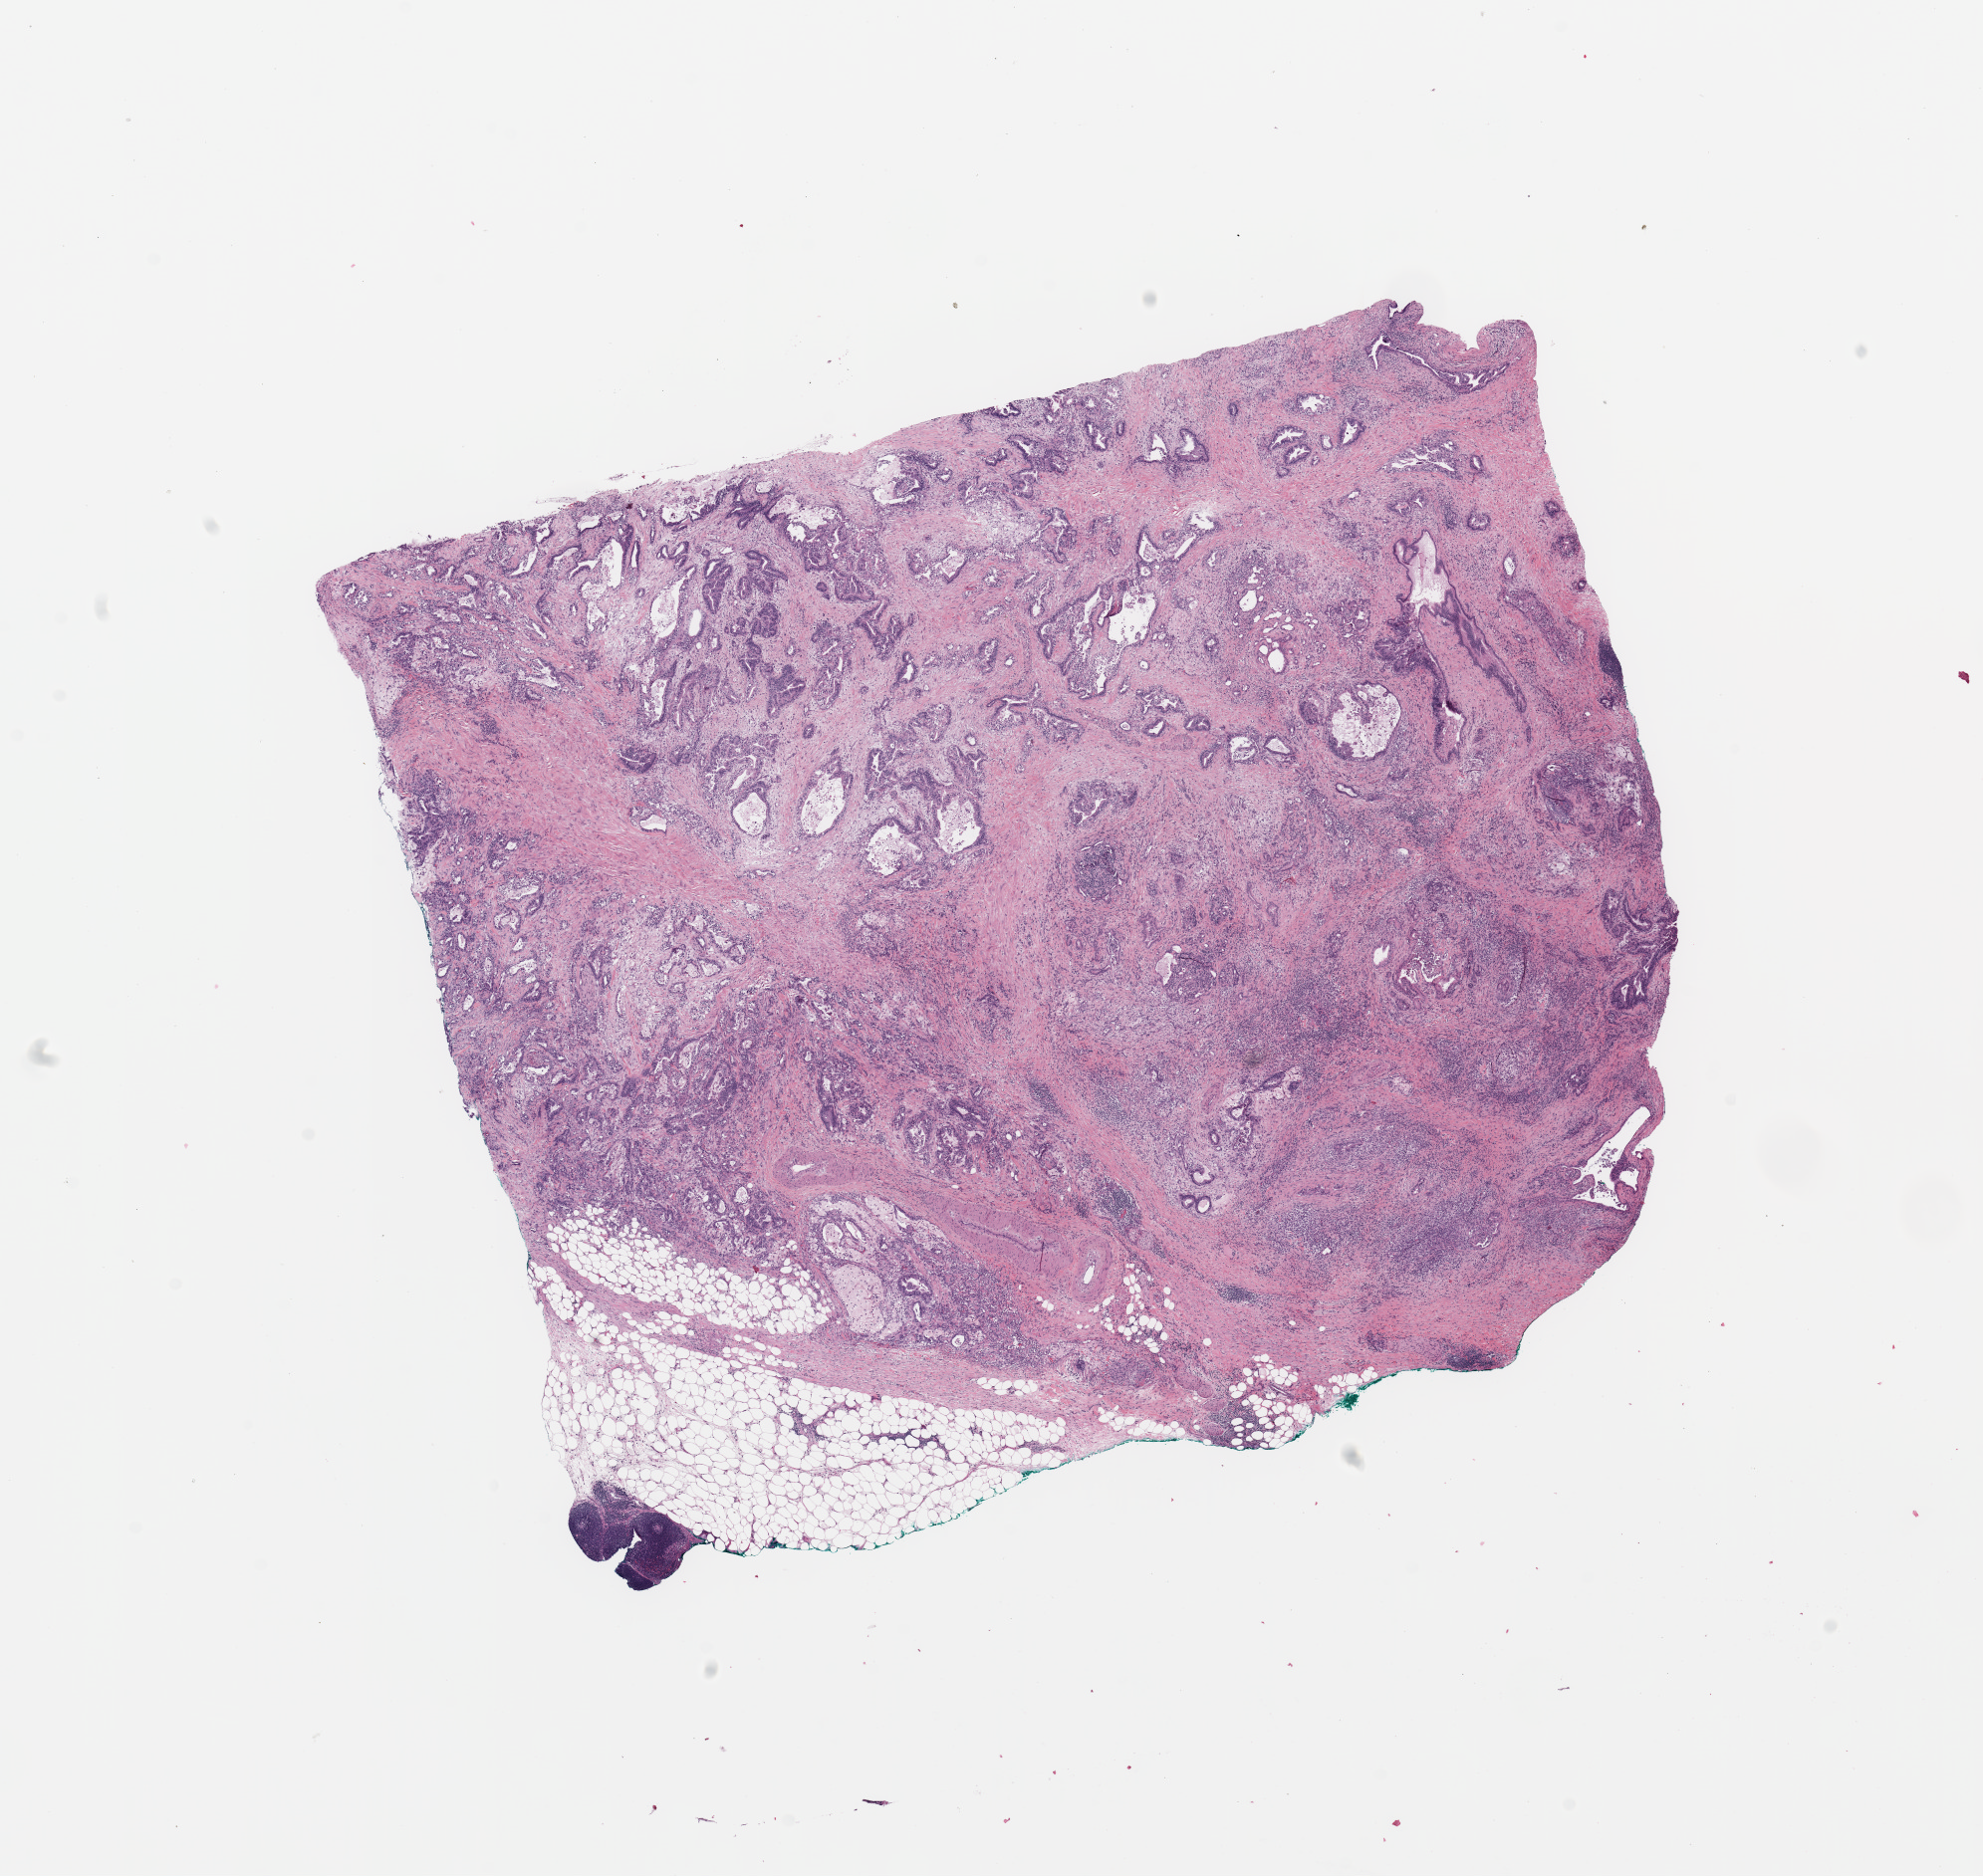
Whole-slide histology image, H&E, whole scanned area (about 15.8 x 14.9 mm) shown as a low-resolution overview, tumour tissue sample, sampled site: pancreas. Patient: male, age 60 years. Histologic grade: G2 (moderately differentiated). Pathologist review of this section (percent, as recorded): tumour nuclei 60%, necrosis 2%.
• primary tumour site (as recorded): head
• AJCC pathologic stage: IIB
• histologic diagnosis: Infiltrating duct carcinoma, NOS